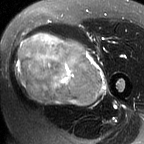
MRI of an extremity soft-tissue mass, one axial slice. Position 31 of 60 along the scan axis. T2-weighted fat-saturated. MR volume resampled by the dataset authors to the PET/CT grid (not the native acquisition matrix). 3.27 mm slice thickness. 144 × 144 image matrix. Female patient. Case-level facts recorded for this patient, not image findings: histological type: pleiomorphic leiomyosarcoma; grade: intermediate; site of the primary tumour: left thigh.
Annotated regions visible in this slice (expert contour drawn on MRI and transferred to this co-registered scan by the dataset authors):
- gross tumour volume including surrounding oedema: box from (x=15, y=33) to (x=106, y=107) px
- gross tumour volume (mass): (x=15, y=33)–(x=103, y=105)